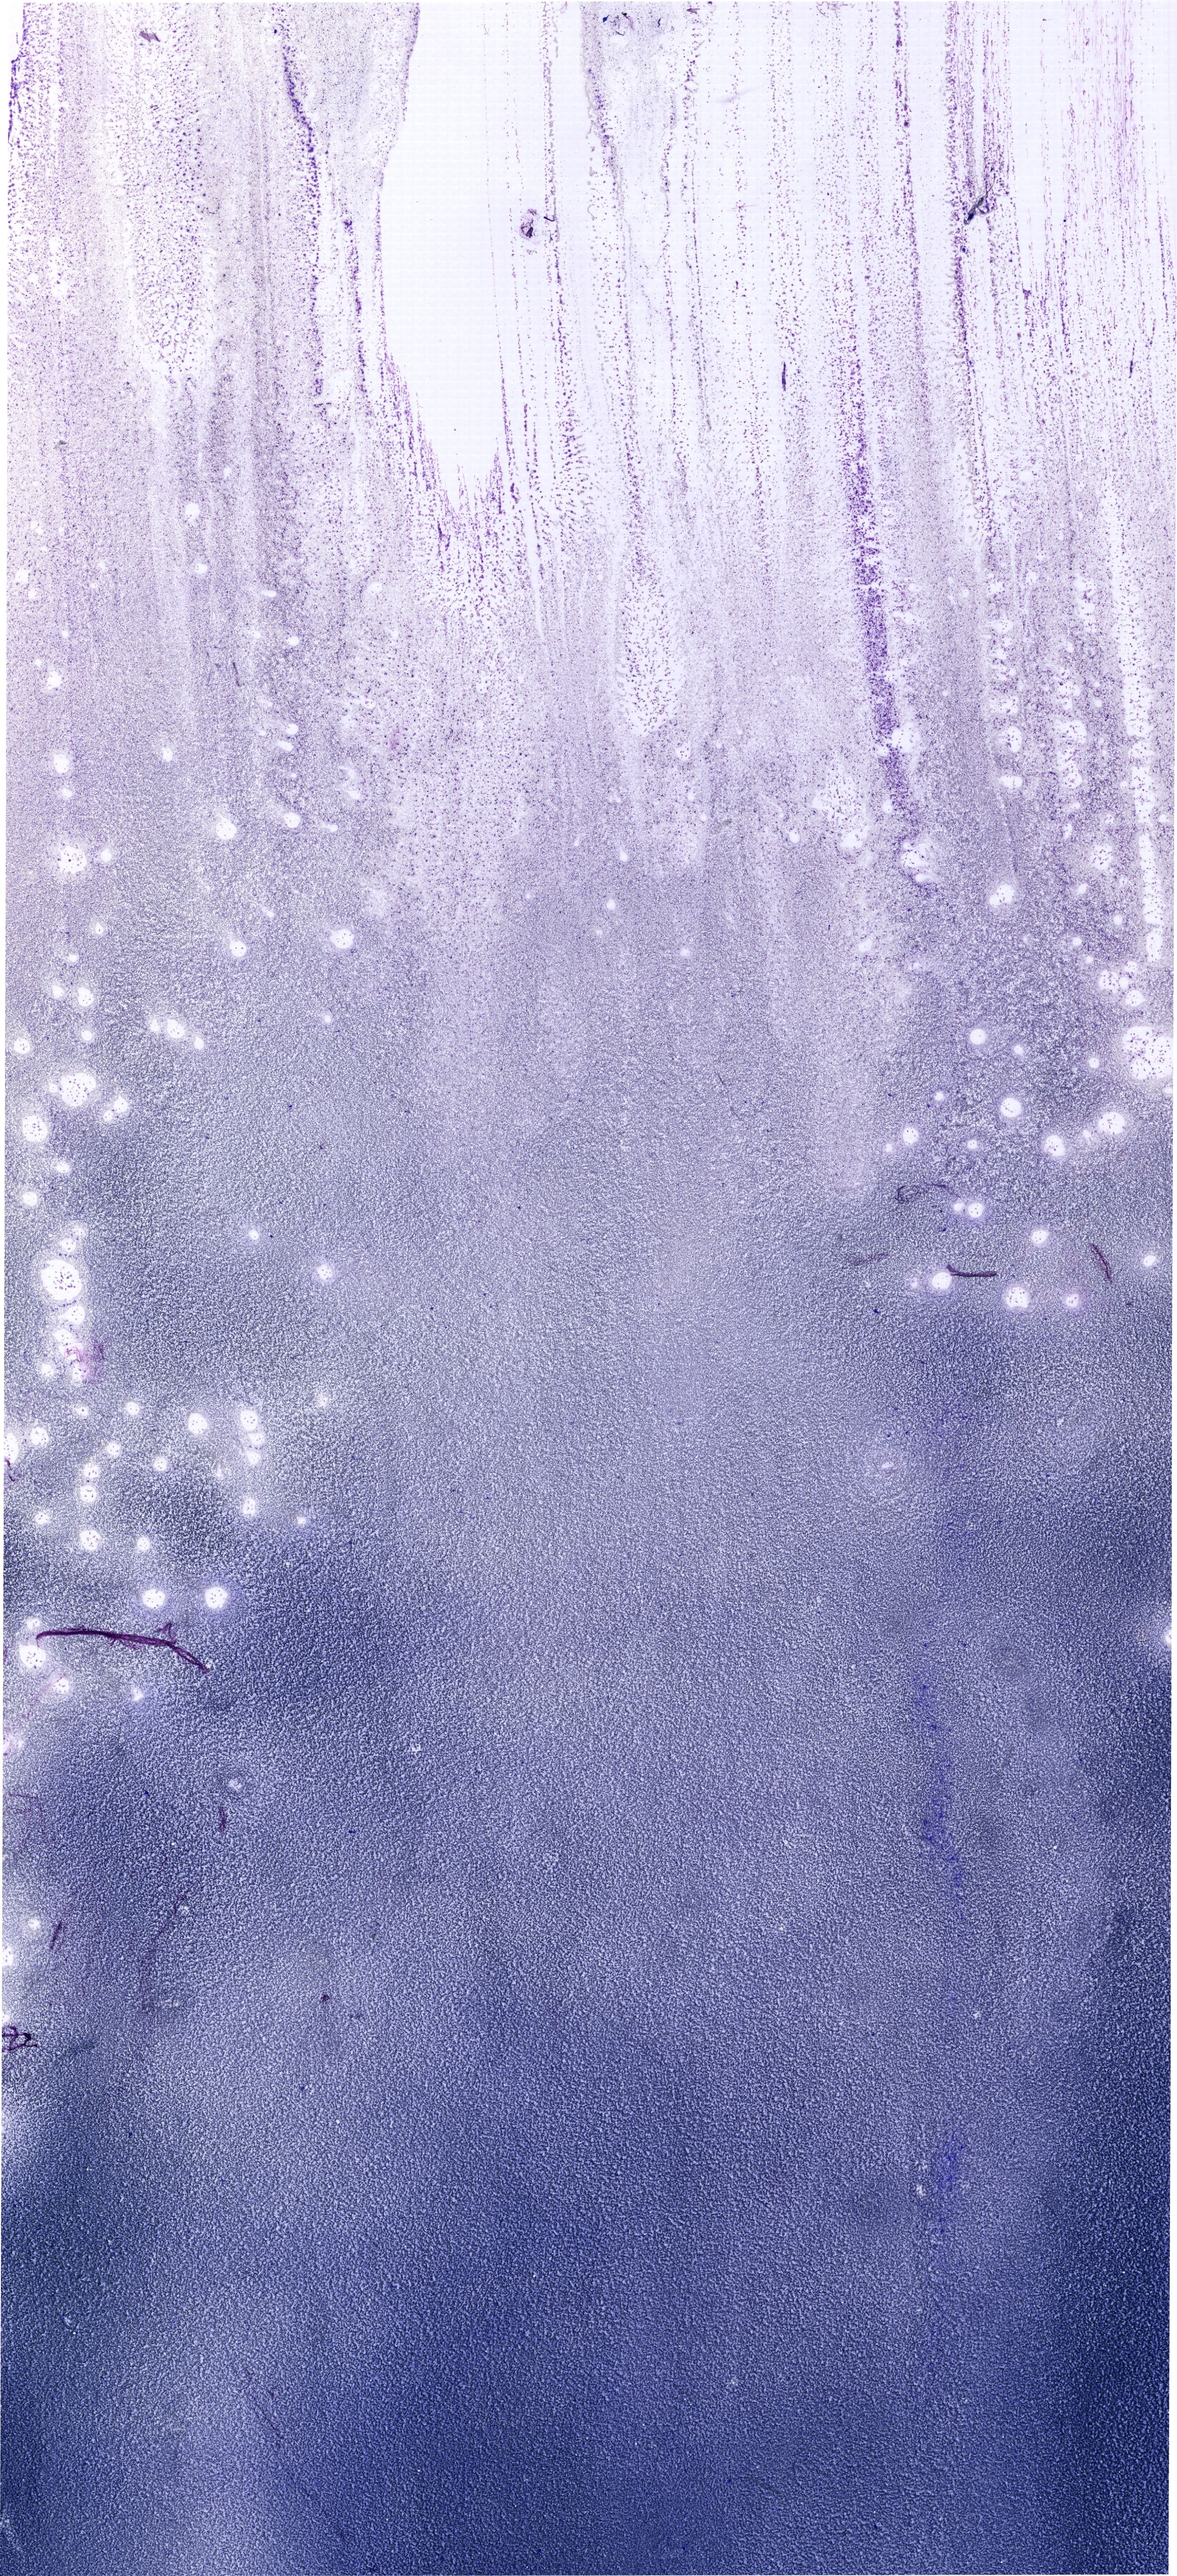
May-Grünwald–Giemsa-stained marrow aspirate smear (whole slide) — a low-resolution overview of the entire scanned area, about 19.9 x 43.6 mm. Female patient.
Diagnosis: Mixed Phenotype Acute Leukemia, B/Myeloid.